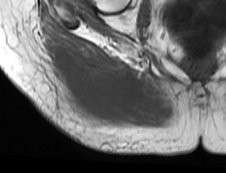
MRI of an extremity soft-tissue mass, one axial slice; slice 28 of 73 in the series (ordered by position); MR volume resampled by the dataset authors to the PET/CT grid (not the native acquisition matrix); 3.27 mm slice thickness; 226 × 173 image matrix, field of view 221 × 169 mm. Female patient. Case-level facts recorded for this patient, not image findings: histological type: spindle cell suggestive of myxofibrosarcoma; grade: intermediate; site of the primary tumour: right buttock.
Outlined on this slice (expert contour drawn on MRI and transferred to this co-registered scan by the dataset authors):
- gross tumour volume (mass): bounding box <45,40,144,128> (left, top, right, bottom; pixels)